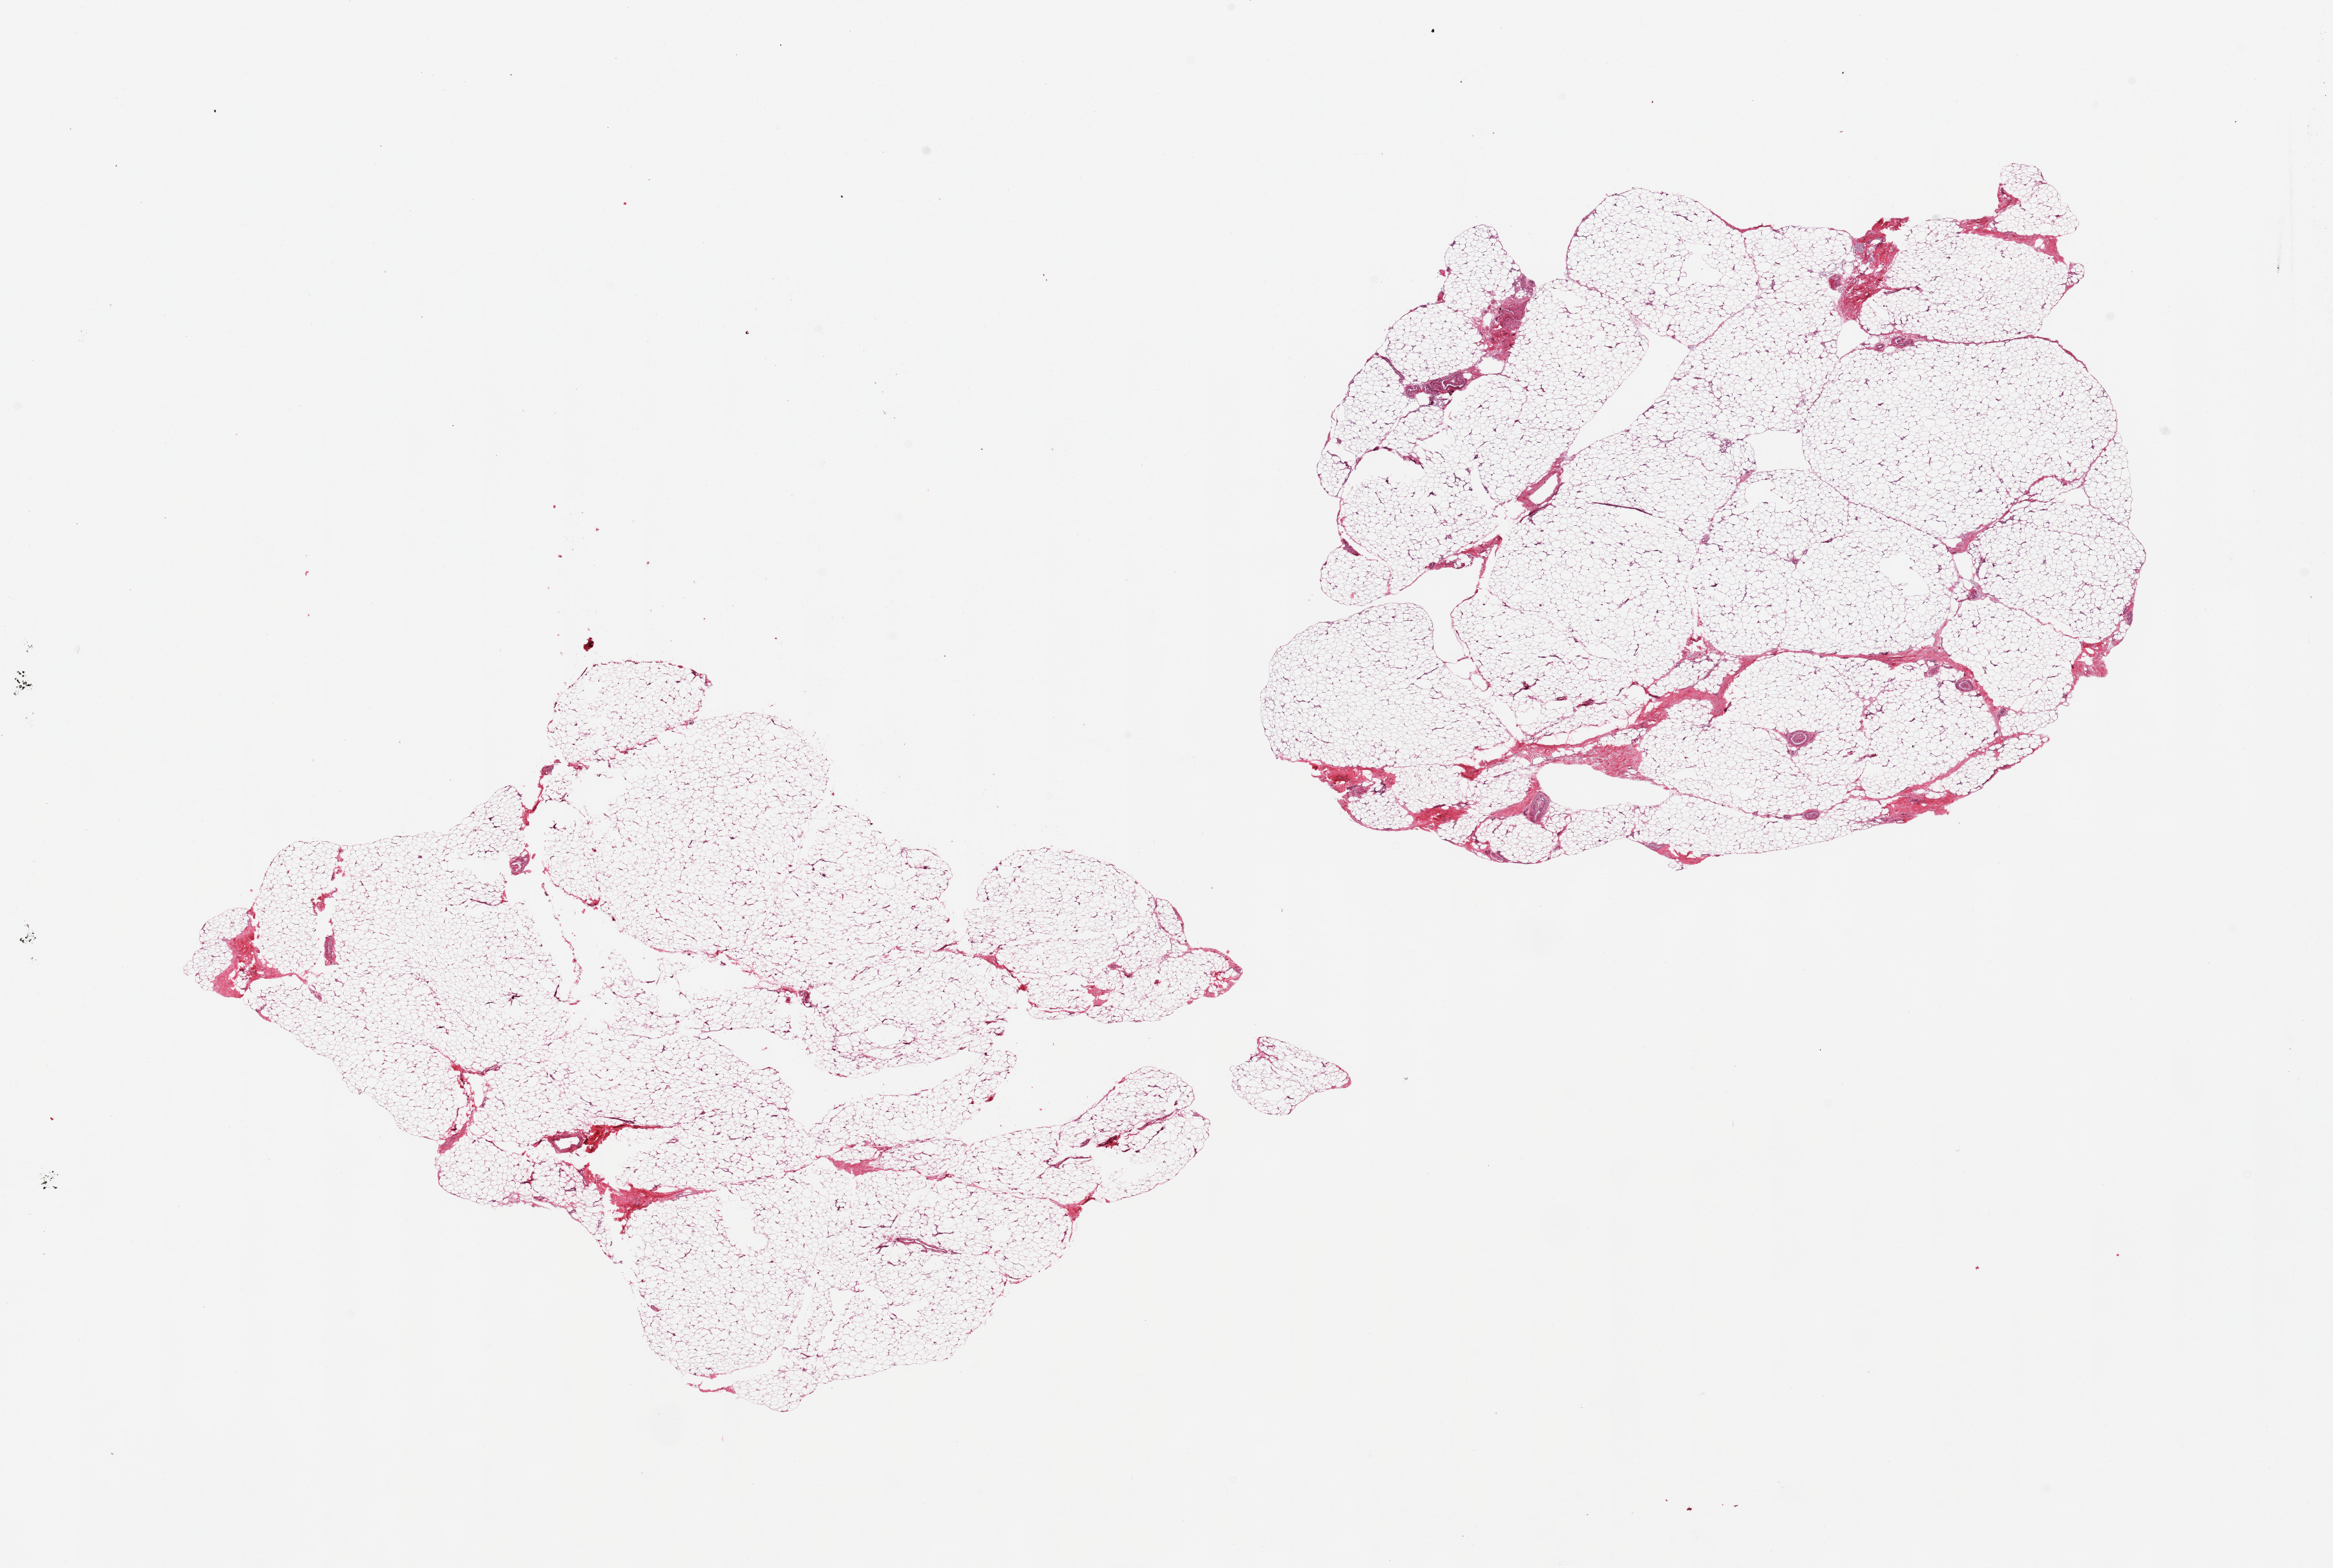
Haematoxylin and eosin whole-slide image, a low-resolution overview of the entire scanned area, about 28.5 x 19.2 mm. PAXgene-fixed paraffin-embedded (PFPE) section. Target tissue: adipose tissue. Donor tissue sample. Donor: male.
- reviewer comment on this tissue sample: 2 pieces, ~5% fascia